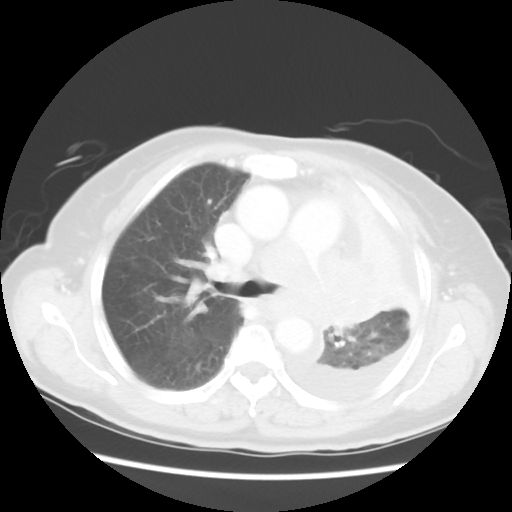
Chest CT, one axial slice. Reconstruction kernel STANDARD. Lung window (W 1500 / L -600 HU). 5 mm slice thickness. 512 × 512 image matrix, field of view 336 × 336 mm. Patient: female, 72 years. Case-level facts recorded for this patient, not image findings: clinical TNM (as recorded): T4 N3 M1b.
Structures marked on this image (bounding box drawn by a radiologist):
- lung tumour (recorded histology: large cell carcinoma): bounding box <301,243,389,341> (left, top, right, bottom; pixels)